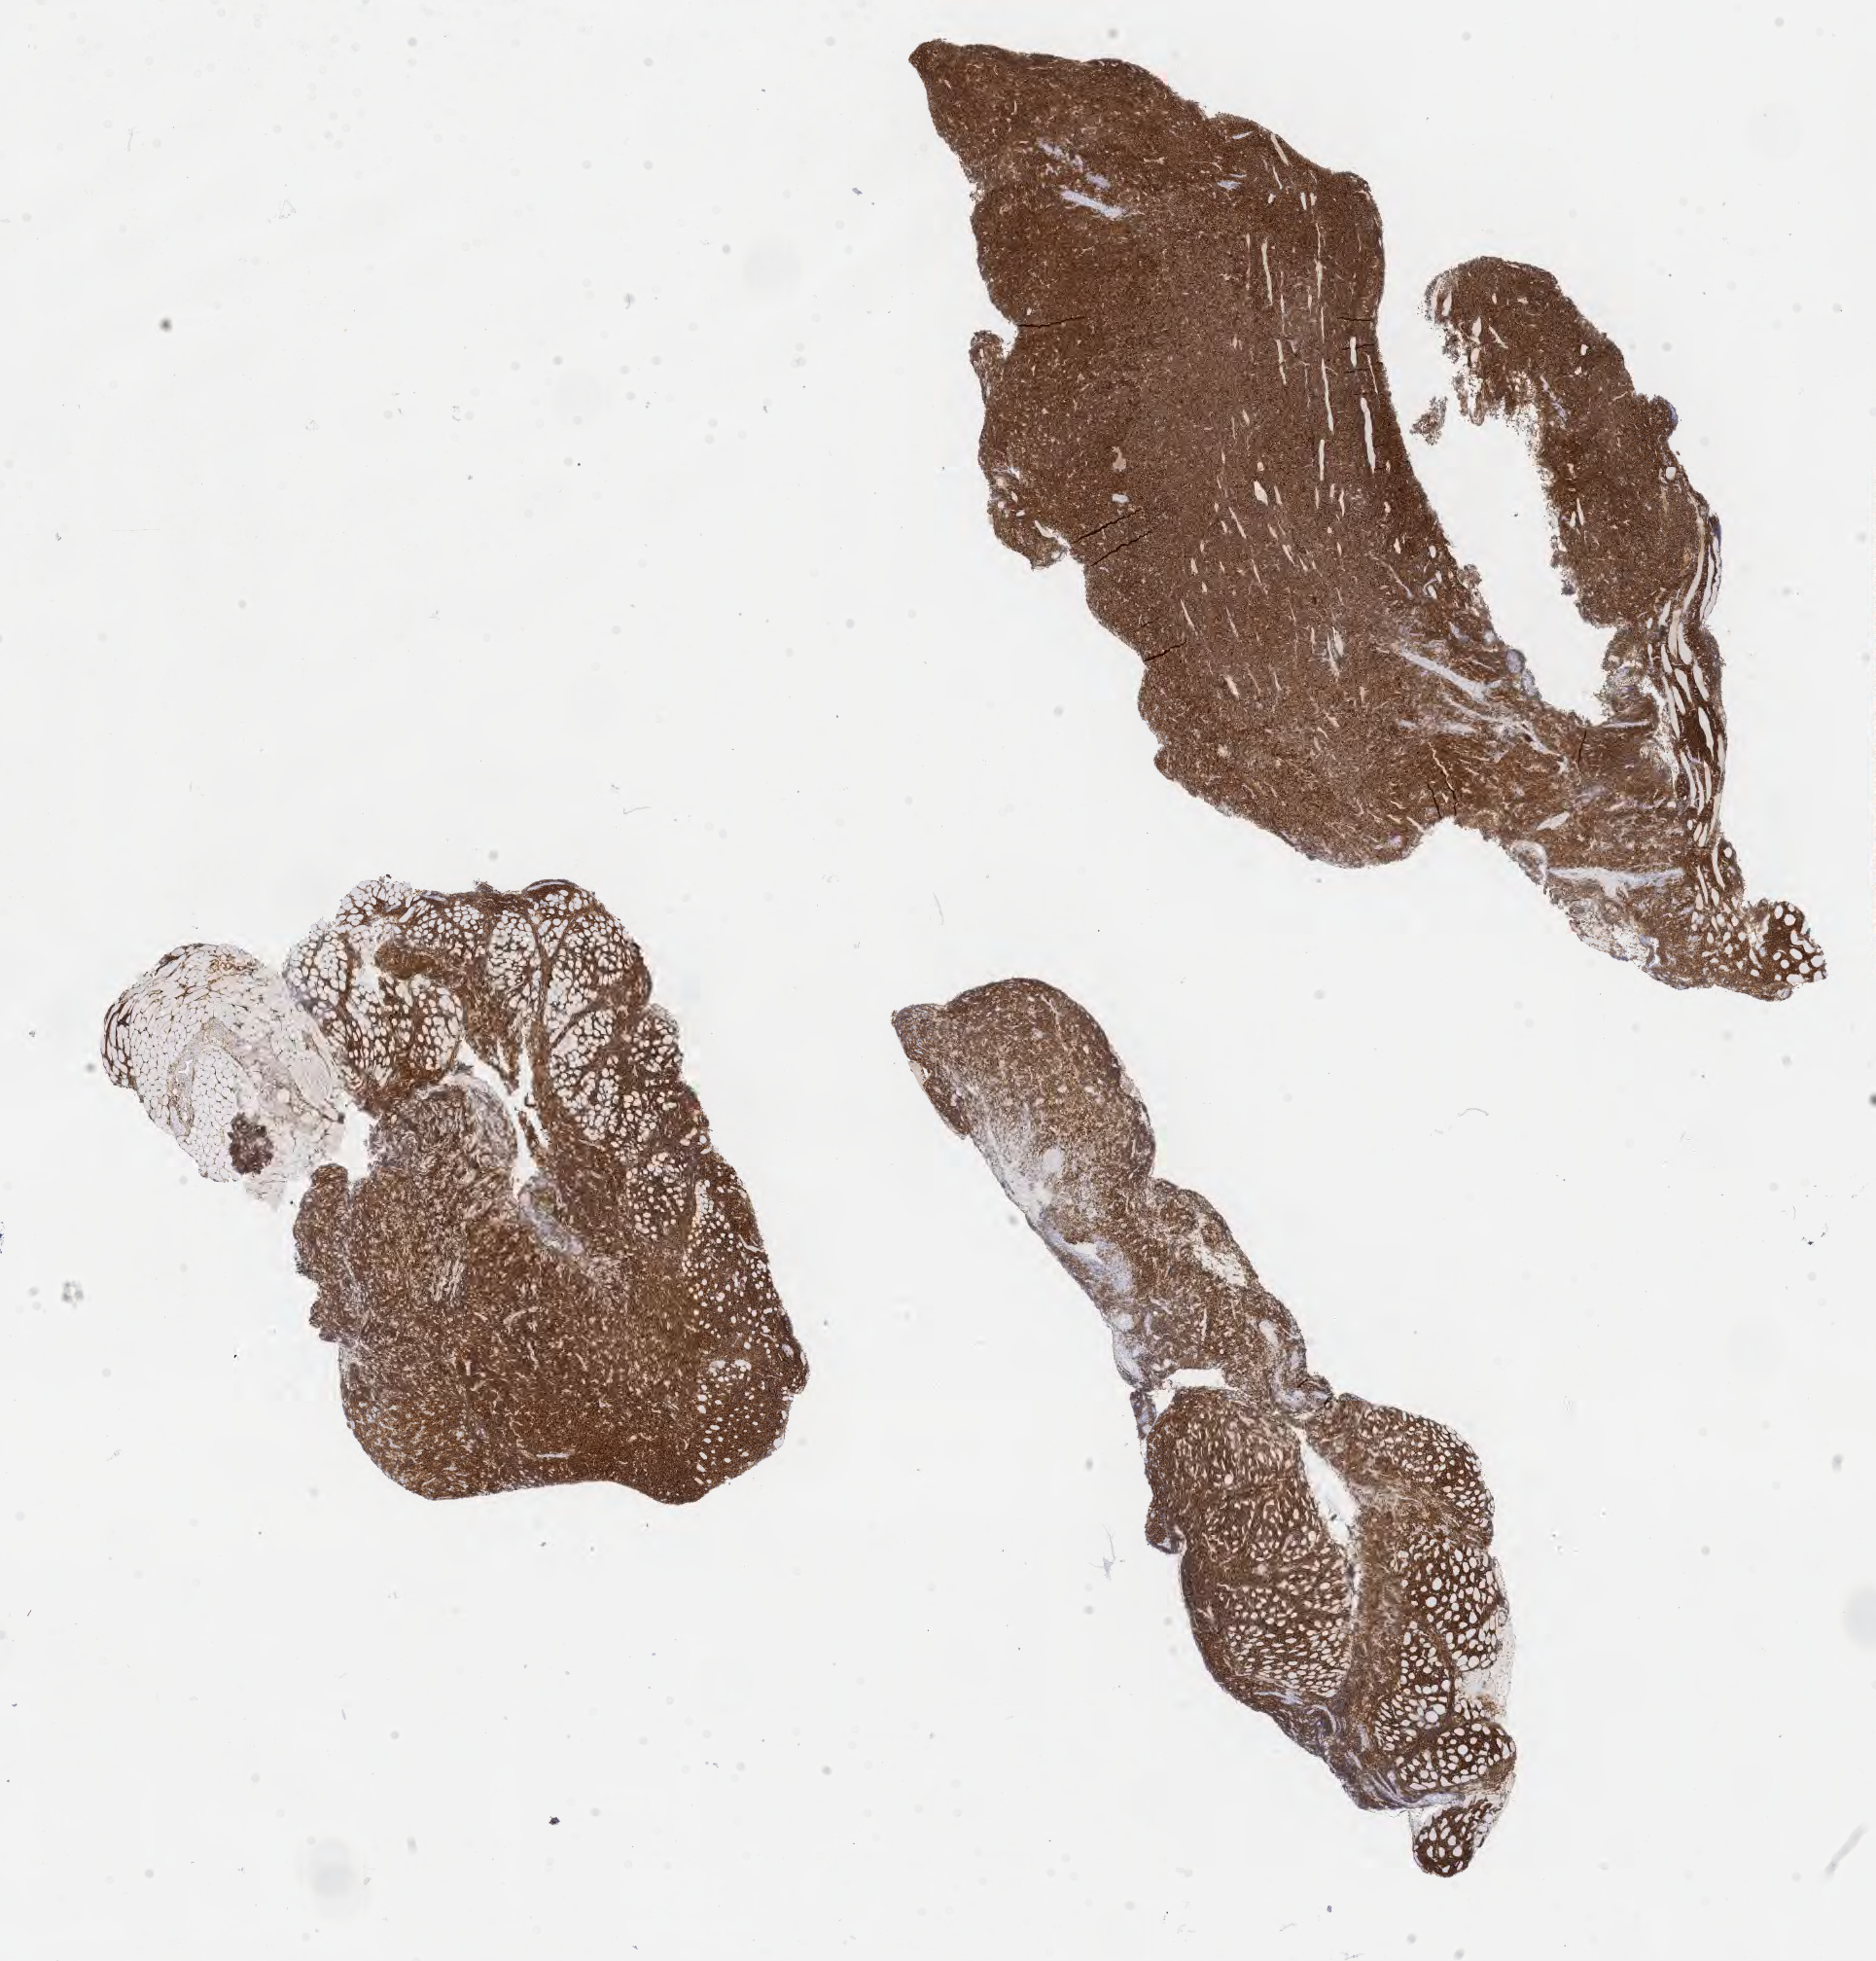
Immunohistochemistry (IHC) whole-slide image stained for CD10, a low-resolution overview of the entire scanned area, about 15.6 x 16.3 mm. Specimen: tumor tissue. Anatomic site: lymph node of head and neck. Patient: male, age 55 years.
Histologic diagnosis: Burkitt lymphoma, NOS.